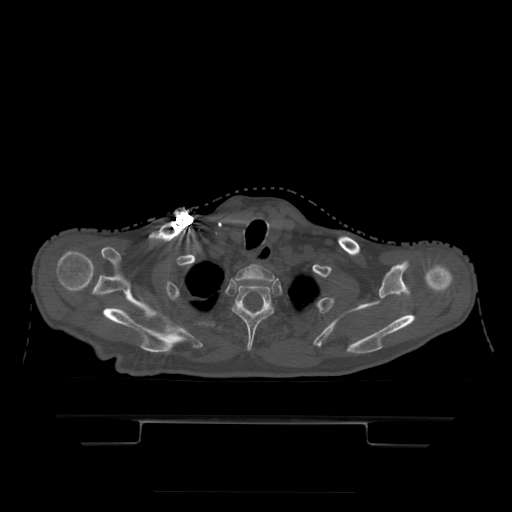
CT including the spine, one axial slice; slice 386 of 522 in the series (ordered by position); bone window (W 1800 / L 400 HU); 512 × 512 image matrix, field of view 436 × 436 mm. Patient age 68 years. Case-level facts recorded for this patient, not image findings: primary cancer: urothelial.
Outlined on this slice (semi-automatic segmentation, software-assisted and operator-edited):
- T1 vertebra: box from (x=235, y=265) to (x=274, y=282) px
- T2 vertebra: (x=233, y=283)–(x=274, y=352)
- T3 vertebra: (x=218, y=306)–(x=266, y=331)